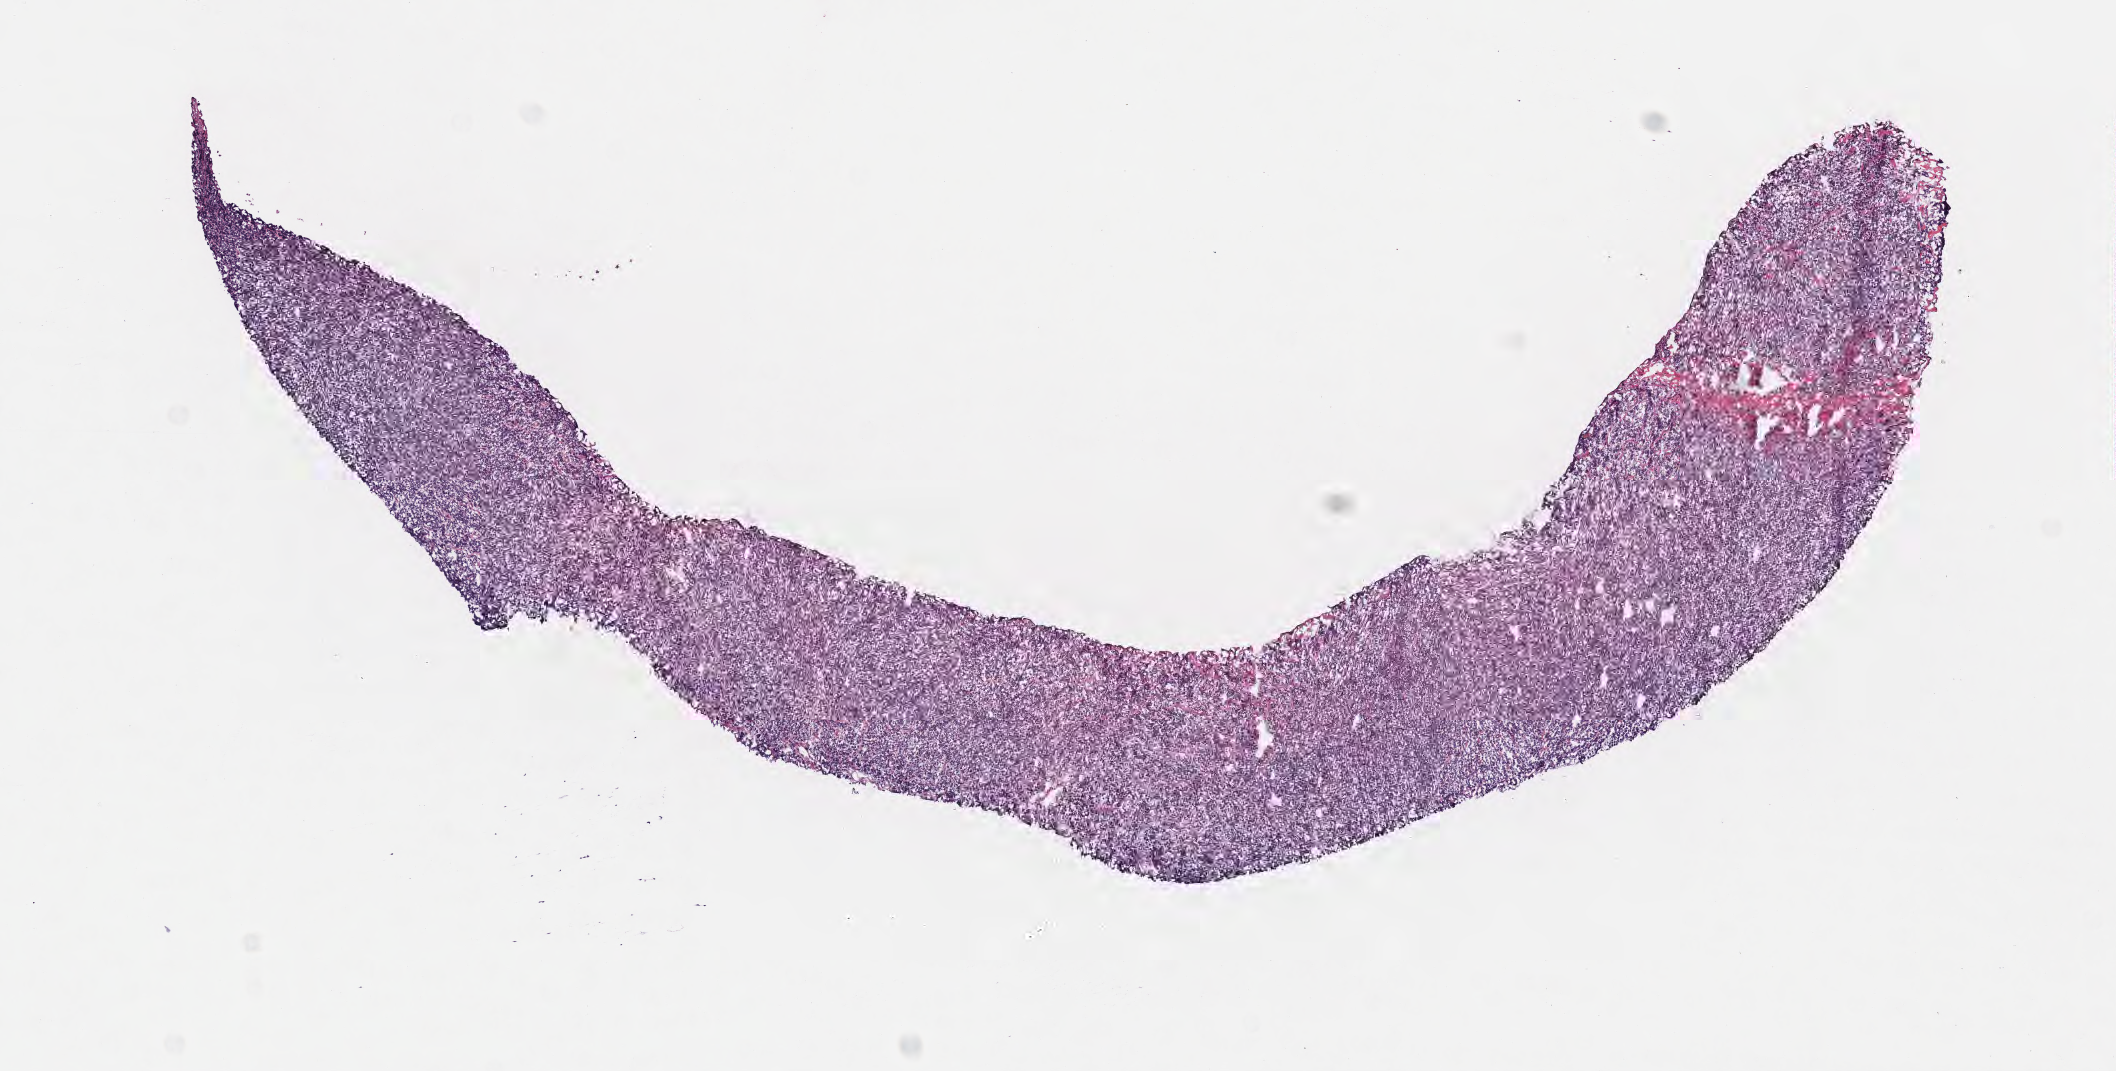
Whole-slide image, H&E stain, a low-resolution overview of the entire scanned area, about 8.6 x 4.3 mm, frozen section (tissue freezing medium), specimen: primary tumor, site: cranium. Patient: male, age at initial diagnosis 5 years. Slide review estimates, as recorded: tumor cells 90%, tumor nuclei 90%, stromal cells 5%, necrosis 5%, normal cells 0%. Infiltration values recorded for this section: lymphocyte infiltration 40%, monocyte infiltration 20%, neutrophil infiltration 20%.
Diagnosis: Burkitt lymphoma, NOS. Section: top of the tissue portion.